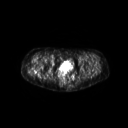
FDG PET of an extremity soft-tissue mass (from a PET/CT study), one axial slice. Slice 52 of 267 in the series (ordered by position). 3.27 mm slice thickness. 128 × 128 image matrix. Patient: female, 57 years. From the clinical record (not read from this slice): histological type: epithelioid sarcoma with vascular differentiation; site of the primary tumour: right buttock.
Annotated regions visible in this slice (expert contour drawn on MRI and transferred to this co-registered scan by the dataset authors):
- gross tumour volume (mass): bounding box [x1, y1, x2, y2] px = [26, 66, 40, 77]